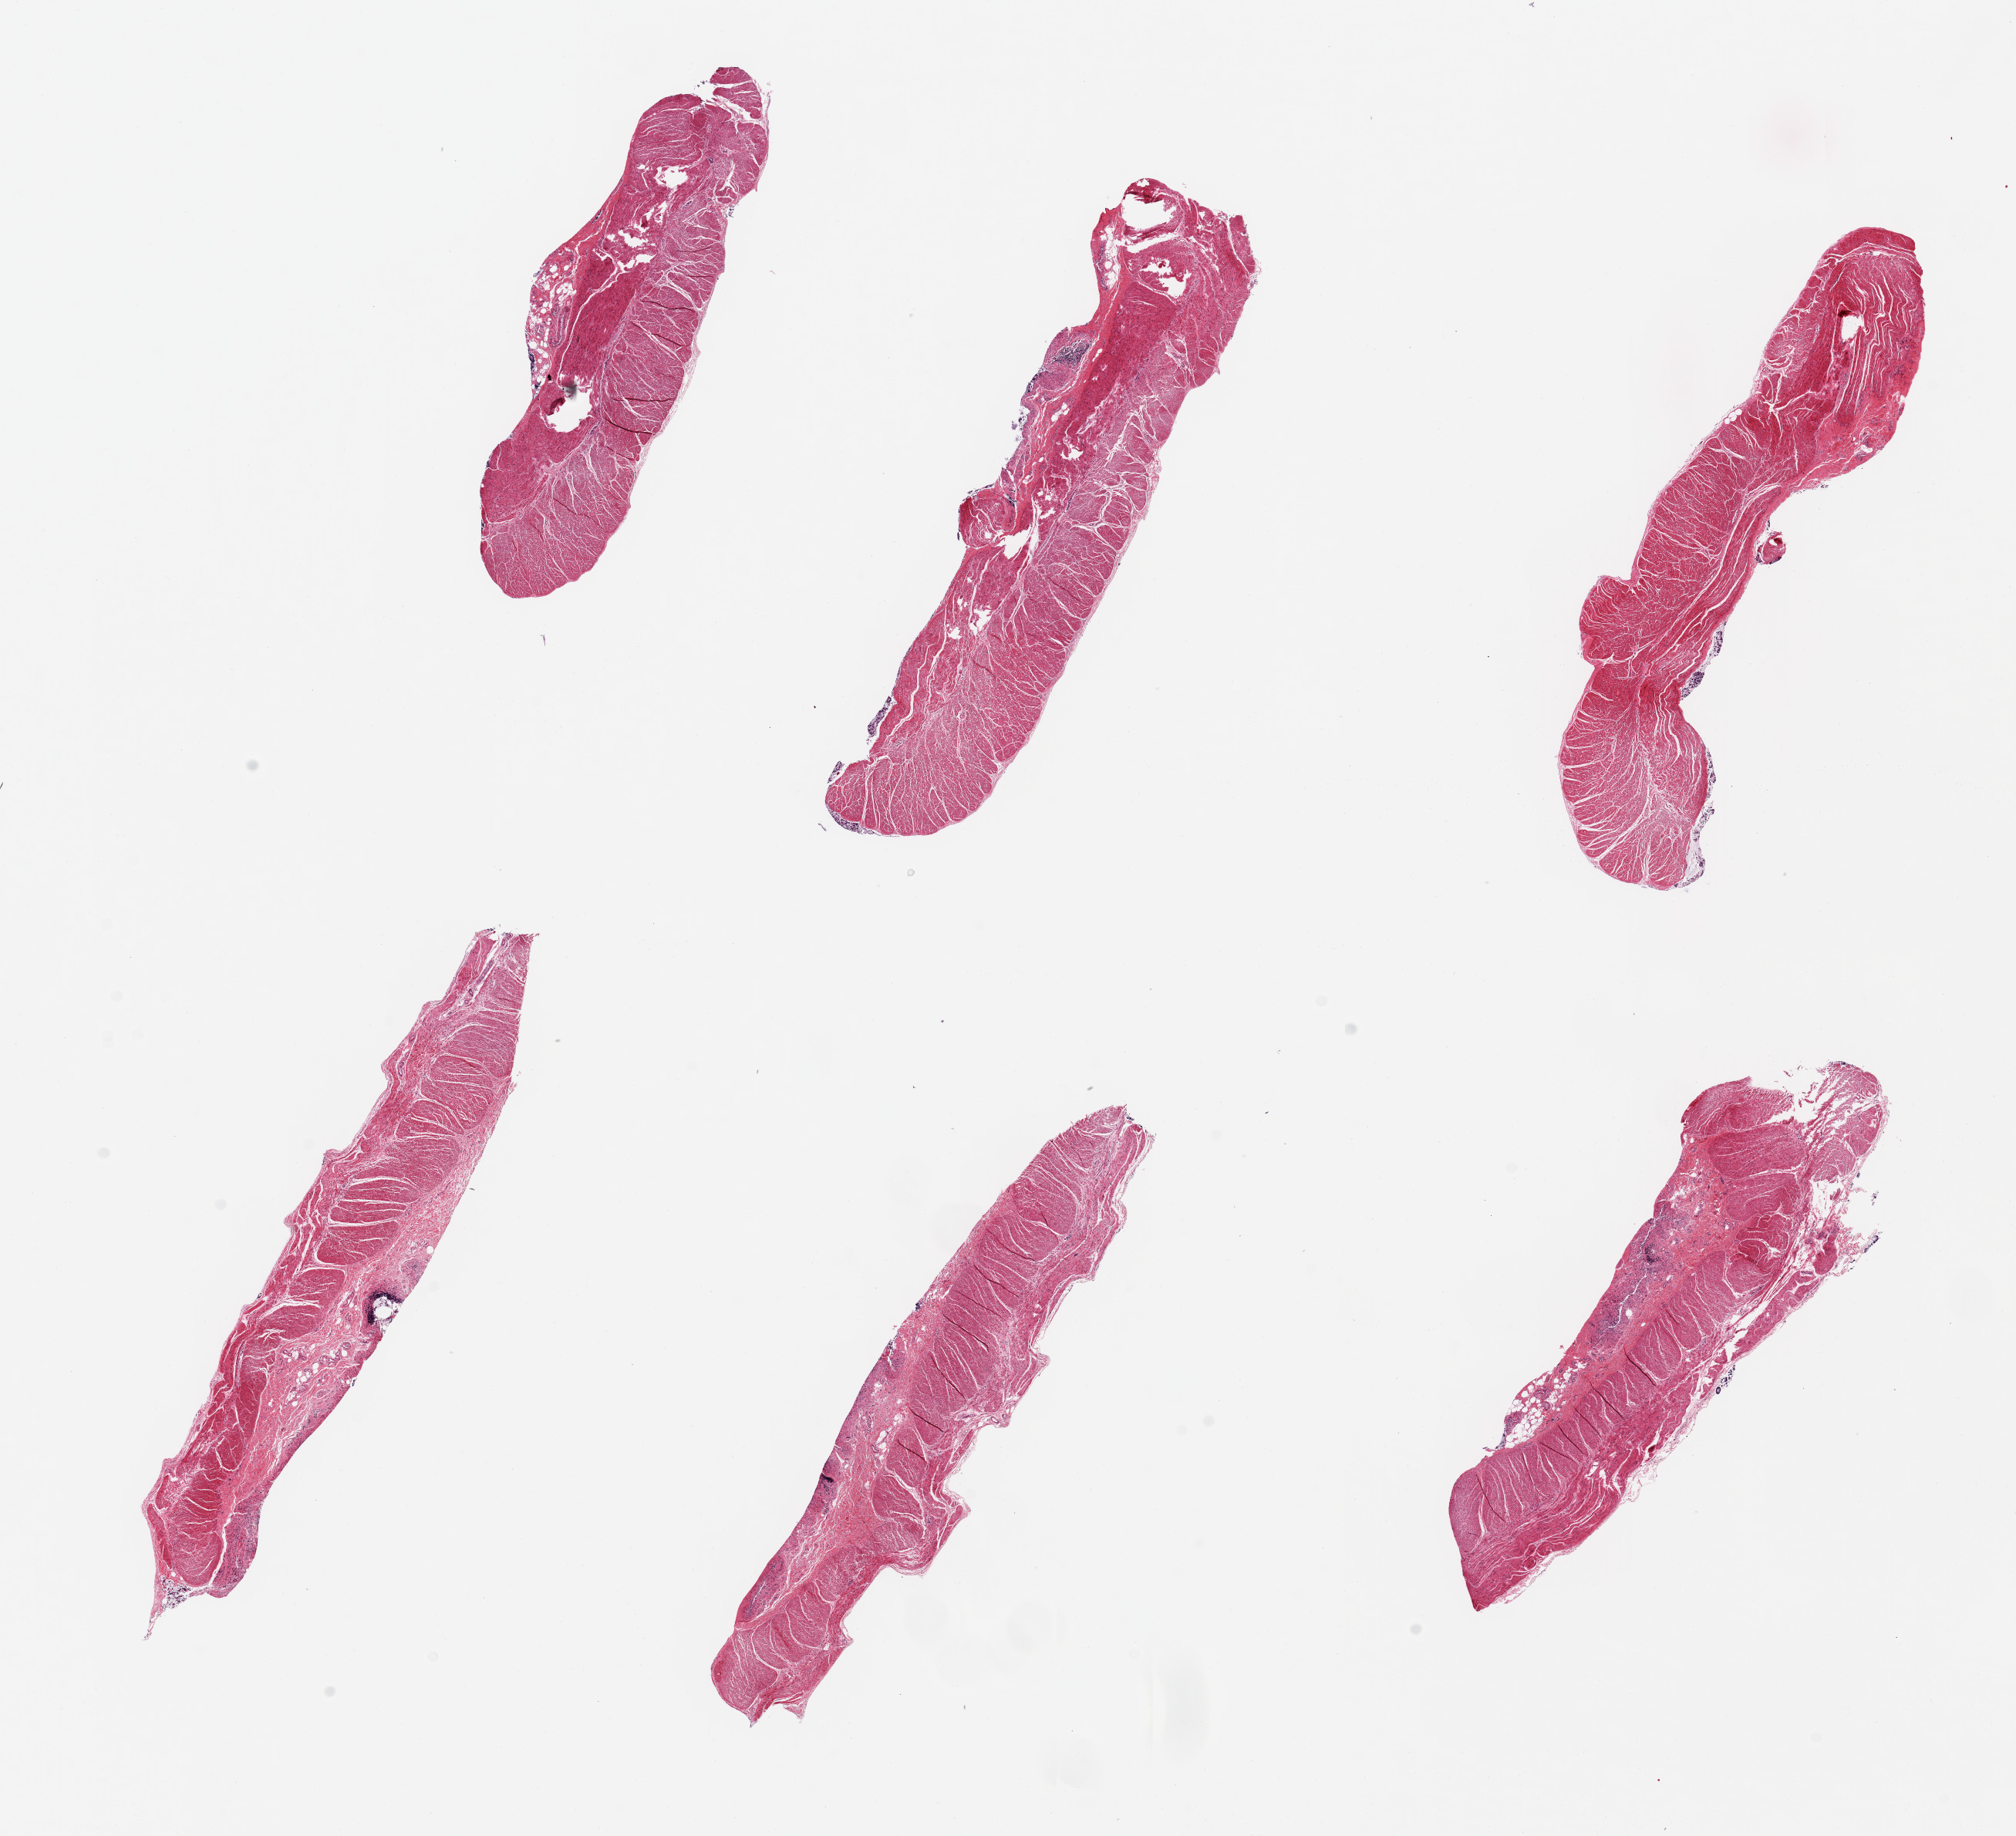
Whole-slide image, haematoxylin and eosin stain — a low-resolution overview of the entire scanned area, about 20.7 x 18.8 mm (slide scanned at 20x). PAXgene-fixed, paraffin-embedded tissue. Section of sigmoid colon (target tissue). Tissue donor sample. Donor: male.
- reviewer comment on this tissue sample: 6 pieces, up to 8x1.5mm; all muscle (target)